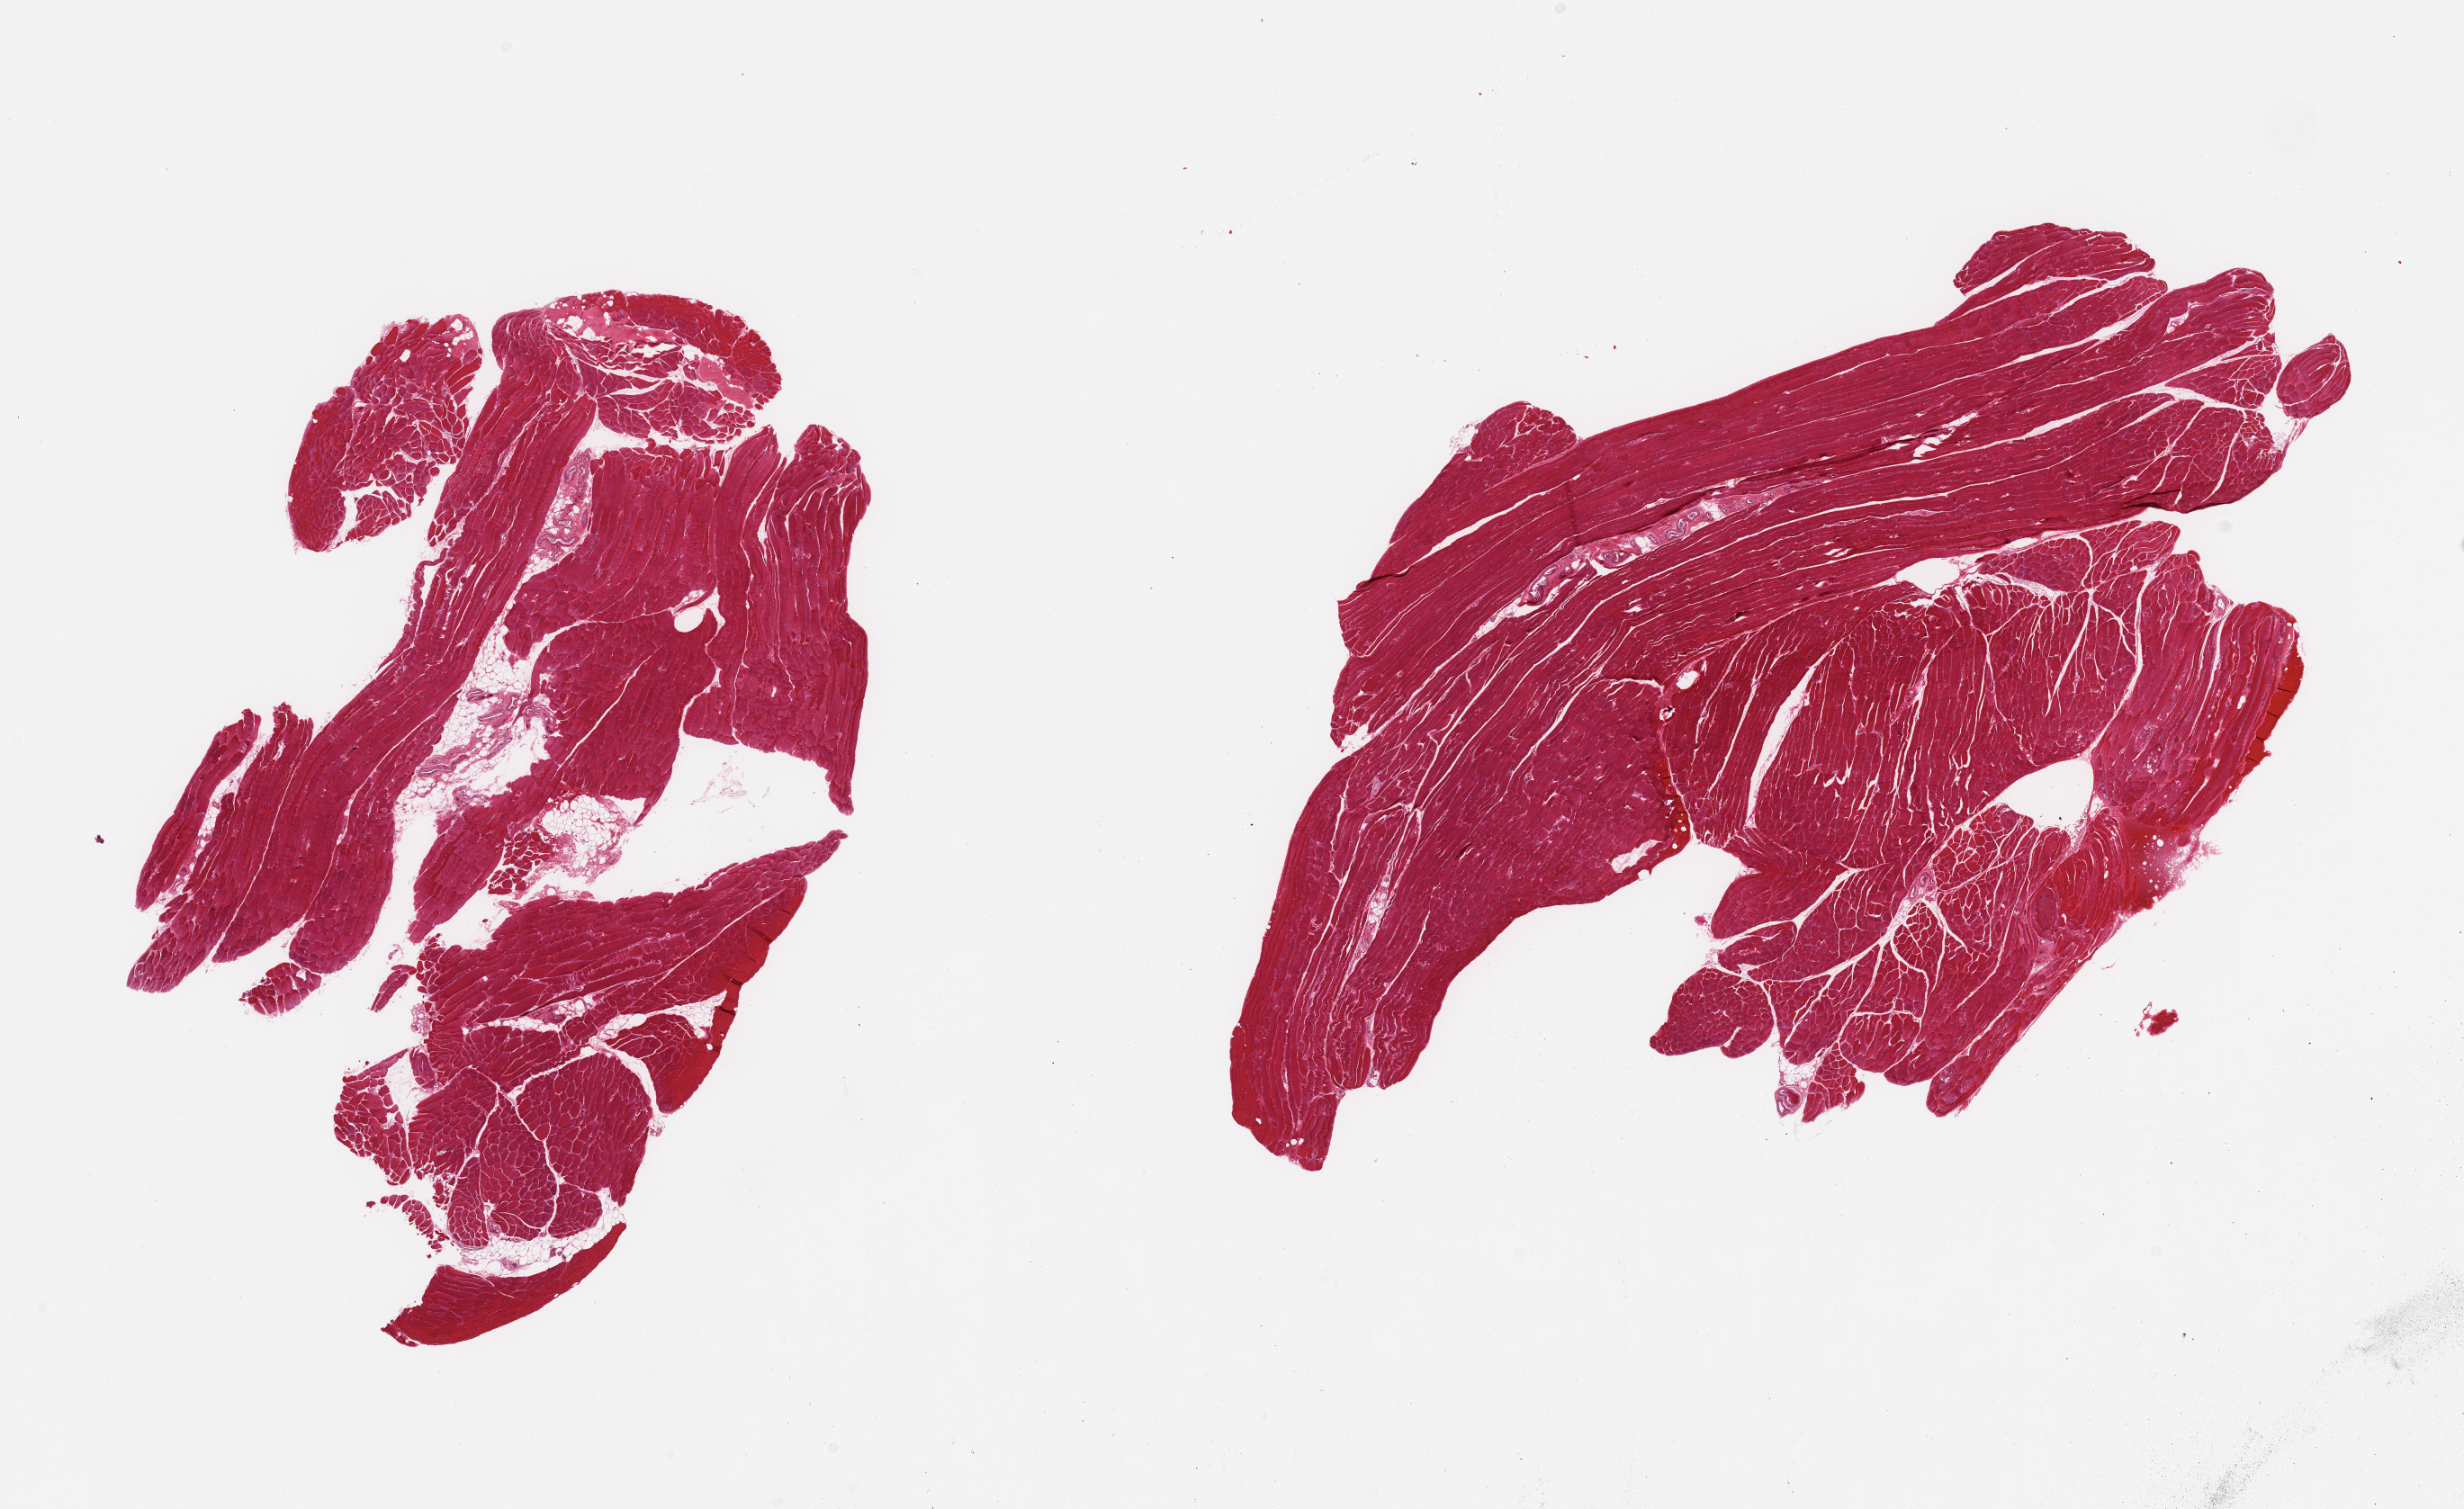
Hematoxylin and eosin (H&E) whole-slide image — shown as a low-resolution overview of the whole scanned area (about 21.7 x 13.3 mm, acquisition: 20x scan), PAXgene-fixed paraffin-embedded (PFPE) section, section of skeletal muscle (target tissue), tissue donor sample. Male donor.
• reviewer comment on this tissue sample: 2 pieces; striations preserved; 5-10% internal fibrovascular content